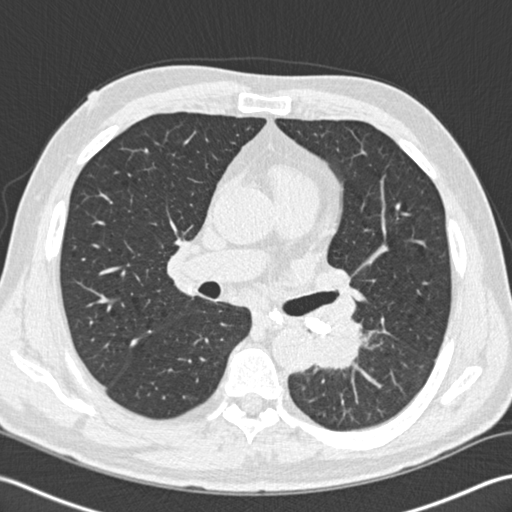
Low-dose screening chest CT, one axial slice; position 100 of 170 along the scan axis; lung window (W 1500 / L -600 HU); 2 mm slice thickness; 512 × 512 image matrix, field of view 350 × 350 mm.
Annotated regions visible in this slice (outlined manually by an expert reader):
- lesion 1 (tumor, lower lobe of left lung): bounding box <315,317,363,369> (left, top, right, bottom; pixels)